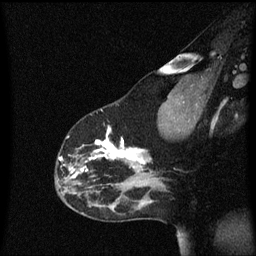
Breast MRI (dynamic contrast-enhanced), one sagittal slice; slice 41 of 60 in the series (ordered by position); dynamic contrast-enhanced series, image 2 of 3 at this slice position (ordered by acquisition); 1.5 T; TE 4.2 ms, TR 8.4 ms; 2 mm slice thickness; 256 × 256 image matrix, field of view 200 × 200 mm. Female patient, age 33 years.
Outlined on this slice (semi-automatically segmented with operator editing):
- analysis volume of interest (the breast-tissue region the enhancement analysis was run in; not a lesion): bounding box [x1, y1, x2, y2] px = [56, 114, 152, 191]
- tumour enhancement mask (voxels above the 70 % enhancement threshold inside the analysis volume of interest): [59, 126, 152, 179]